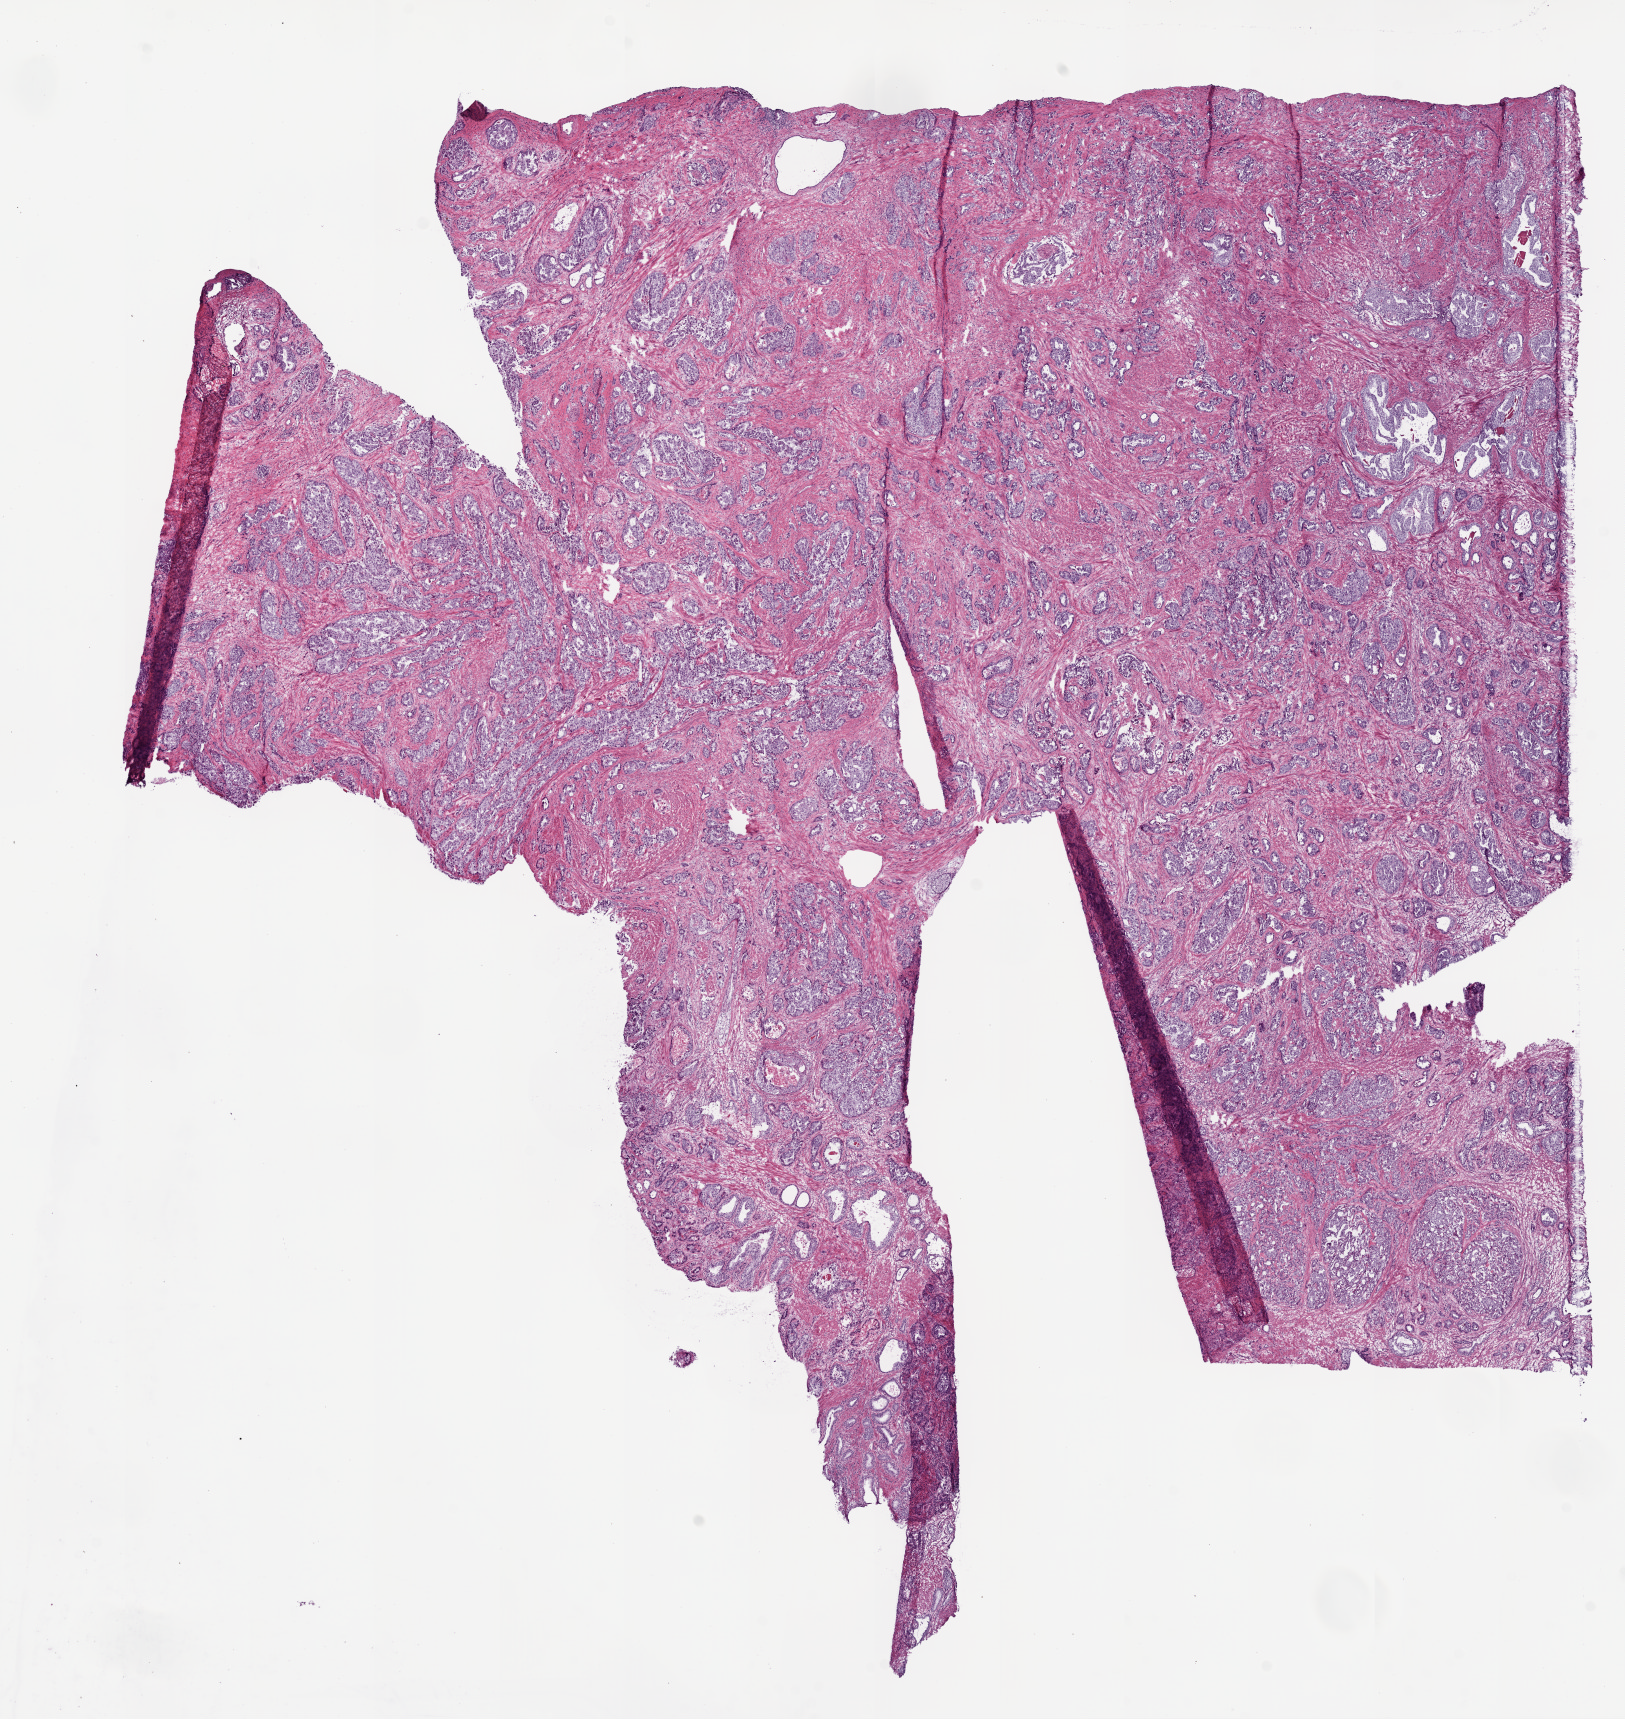
Digitized H&E tissue section (whole slide) — whole scanned area (about 13.0 x 13.8 mm, acquisition: 20x scan) shown as a low-resolution overview, frozen section from the bottom of the tissue portion, sample: primary tumour, prostate. Patient: male, age at initial diagnosis 66 years. Composition of this section per pathologist review: tumour cells 55%, tumour nuclei 65%.
Diagnosis: Acinar cell carcinoma (prostate gland).